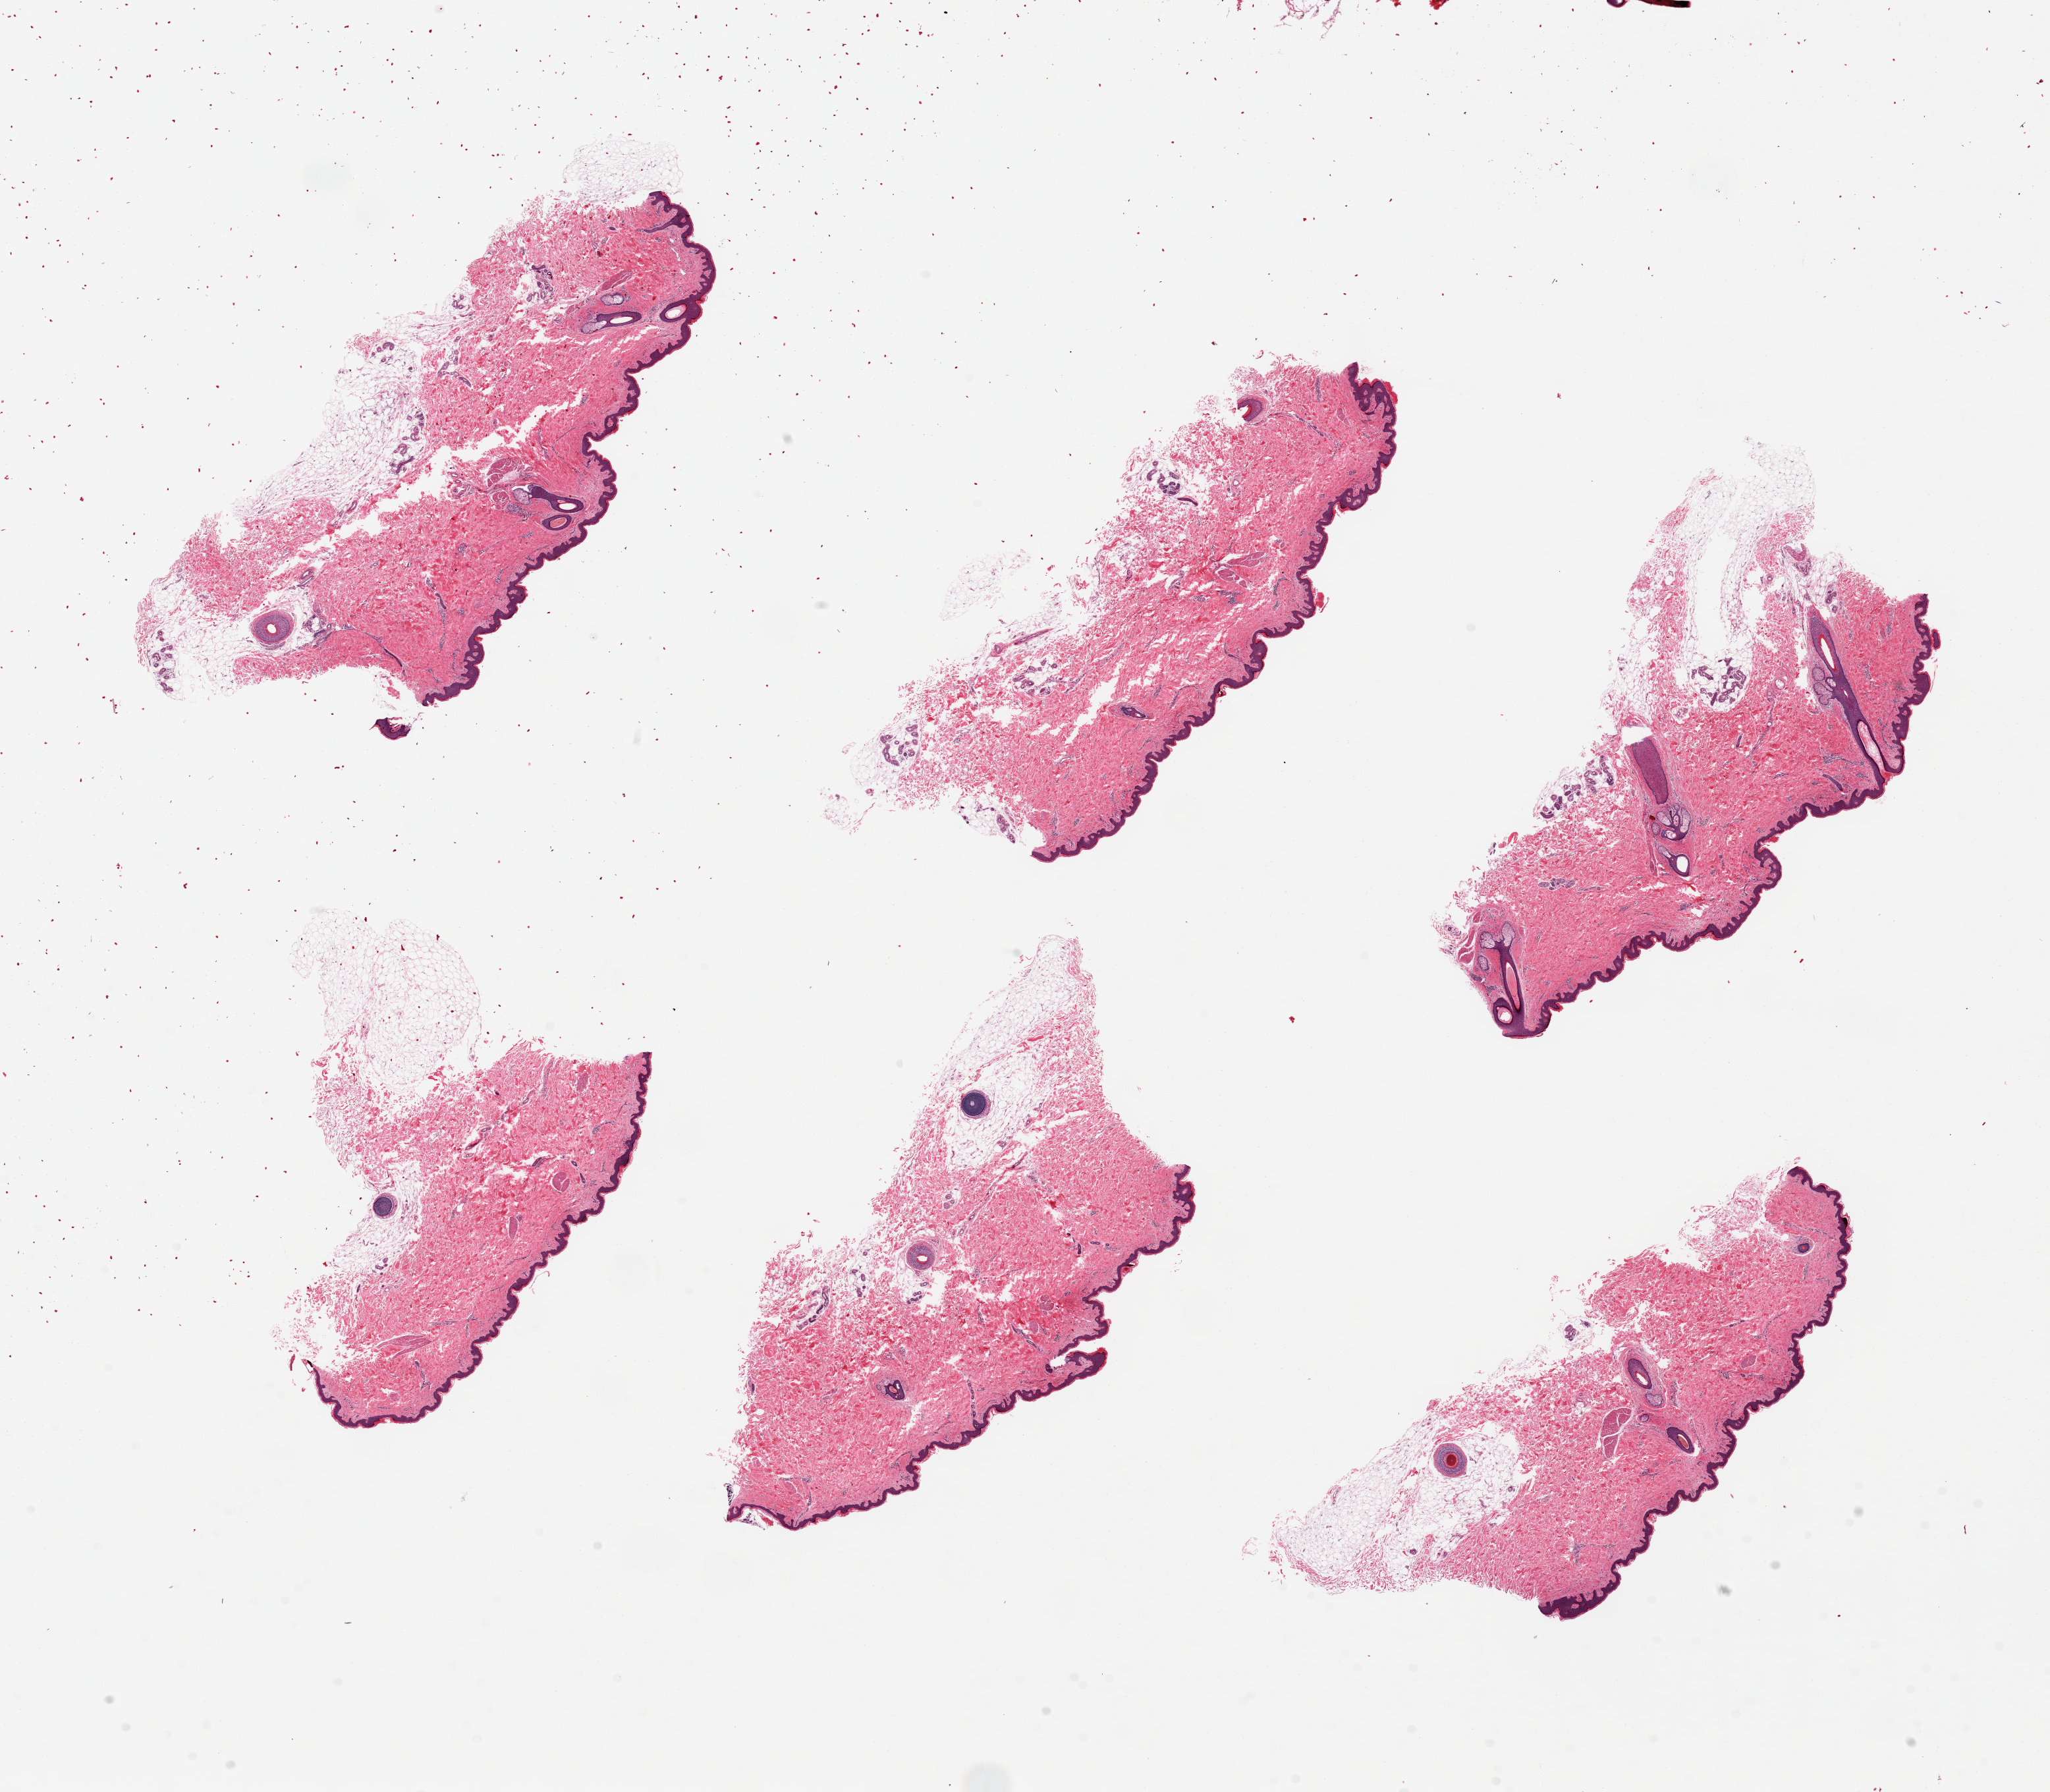
Digitized hematoxylin and eosin (H&E)-stained section, a low-resolution overview of the entire scanned area, about 24.6 x 21.5 mm. PAXgene-fixed paraffin-embedded (PFPE) section. Sampled site (target tissue): skin of suprapubic region. Donor tissue sample. Male donor.
* pathologist's review note for this sample: 6 pieces, up to 9x4mm; up to 2 mm thick band of subcutaneous adipose tissue